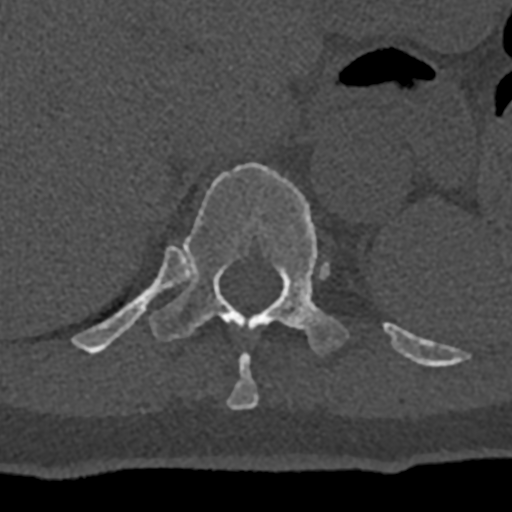
CT including the spine, one axial slice. Reconstruction kernel Br40s/3. Bone window (W 1800 / L 400 HU). 0.5 mm slice thickness. 512 × 512 image matrix, field of view 160 × 160 mm. Patient: male, 74 years. From the clinical record (not read from this slice): primary cancer: renal; vertebrae with lytic lesions (as recorded): T10, L1, L2, L3, L4, L5.
Structures marked on this image (semi-automatically segmented with operator editing):
- T10 vertebra: bounding box (x1, y1, x2, y2) in pixels: (226, 352, 259, 409)
- T11 vertebra: (72, 163, 432, 367)